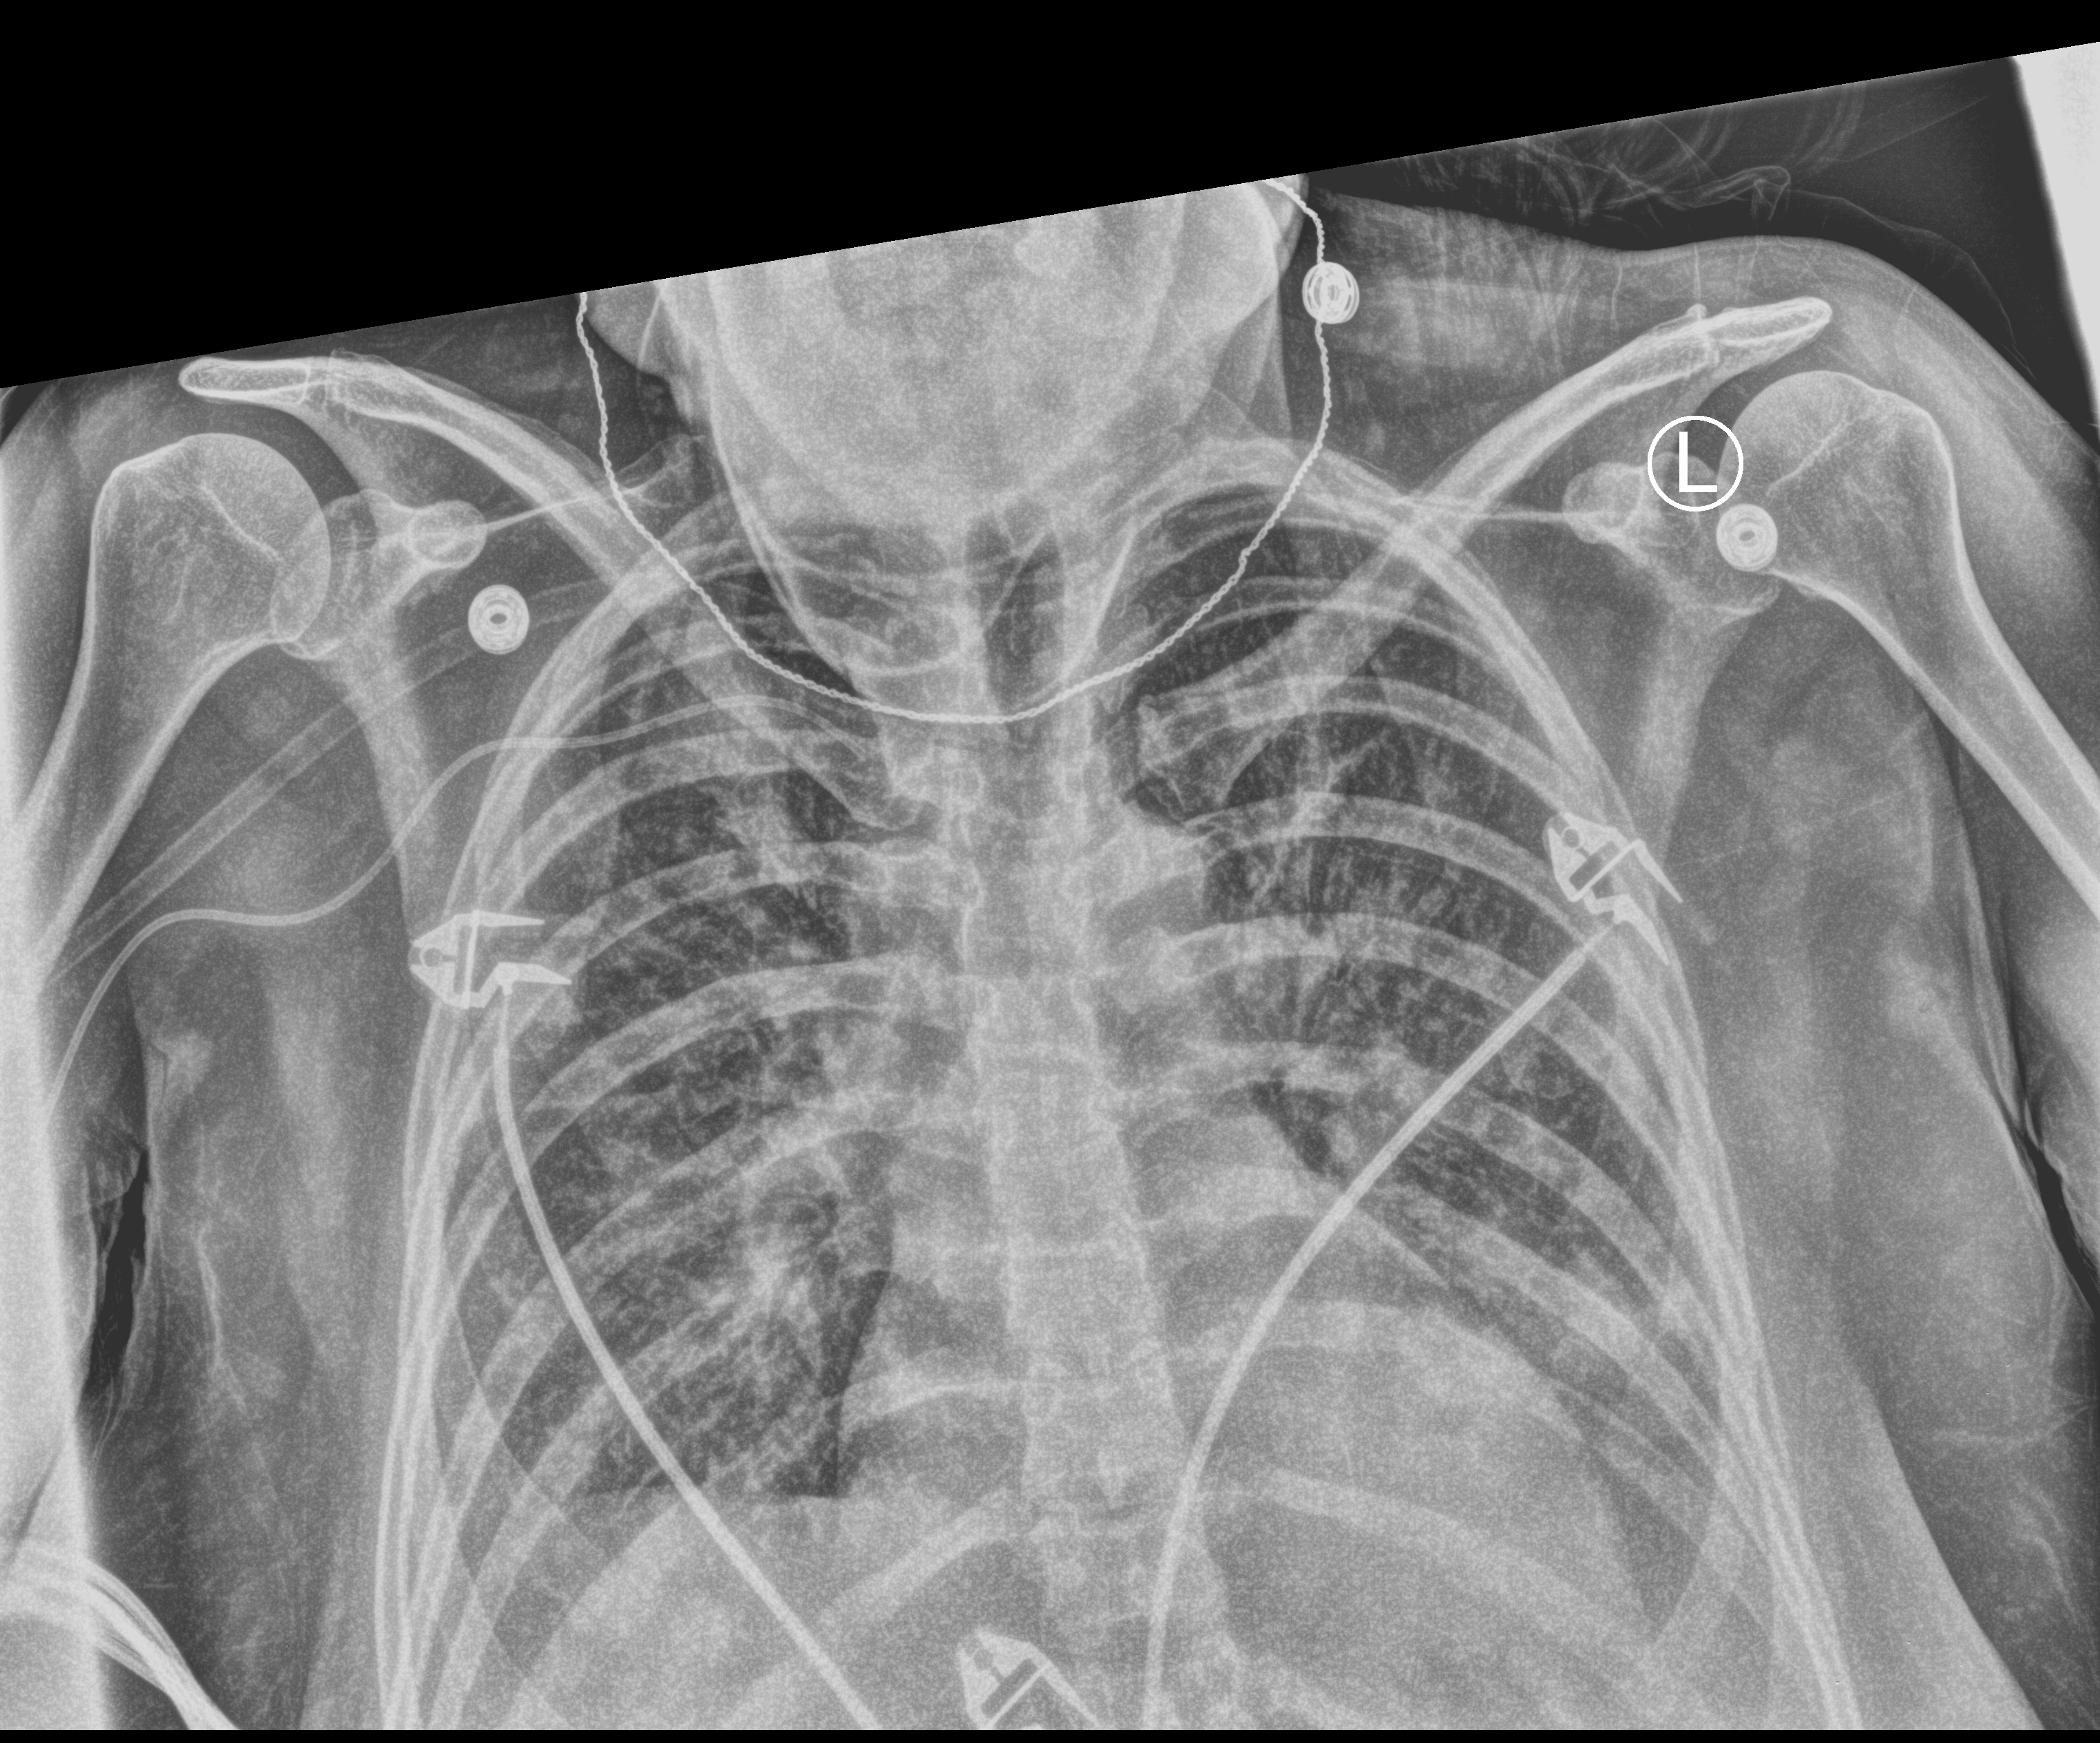
Chest X-ray (portable); anteroposterior (AP) projection. Female patient hospitalised with COVID-19, age 18–59 years.
Admission-level facts for this patient (not findings on this image; timing relative to this image not recorded):
- length of hospital stay: 13 days